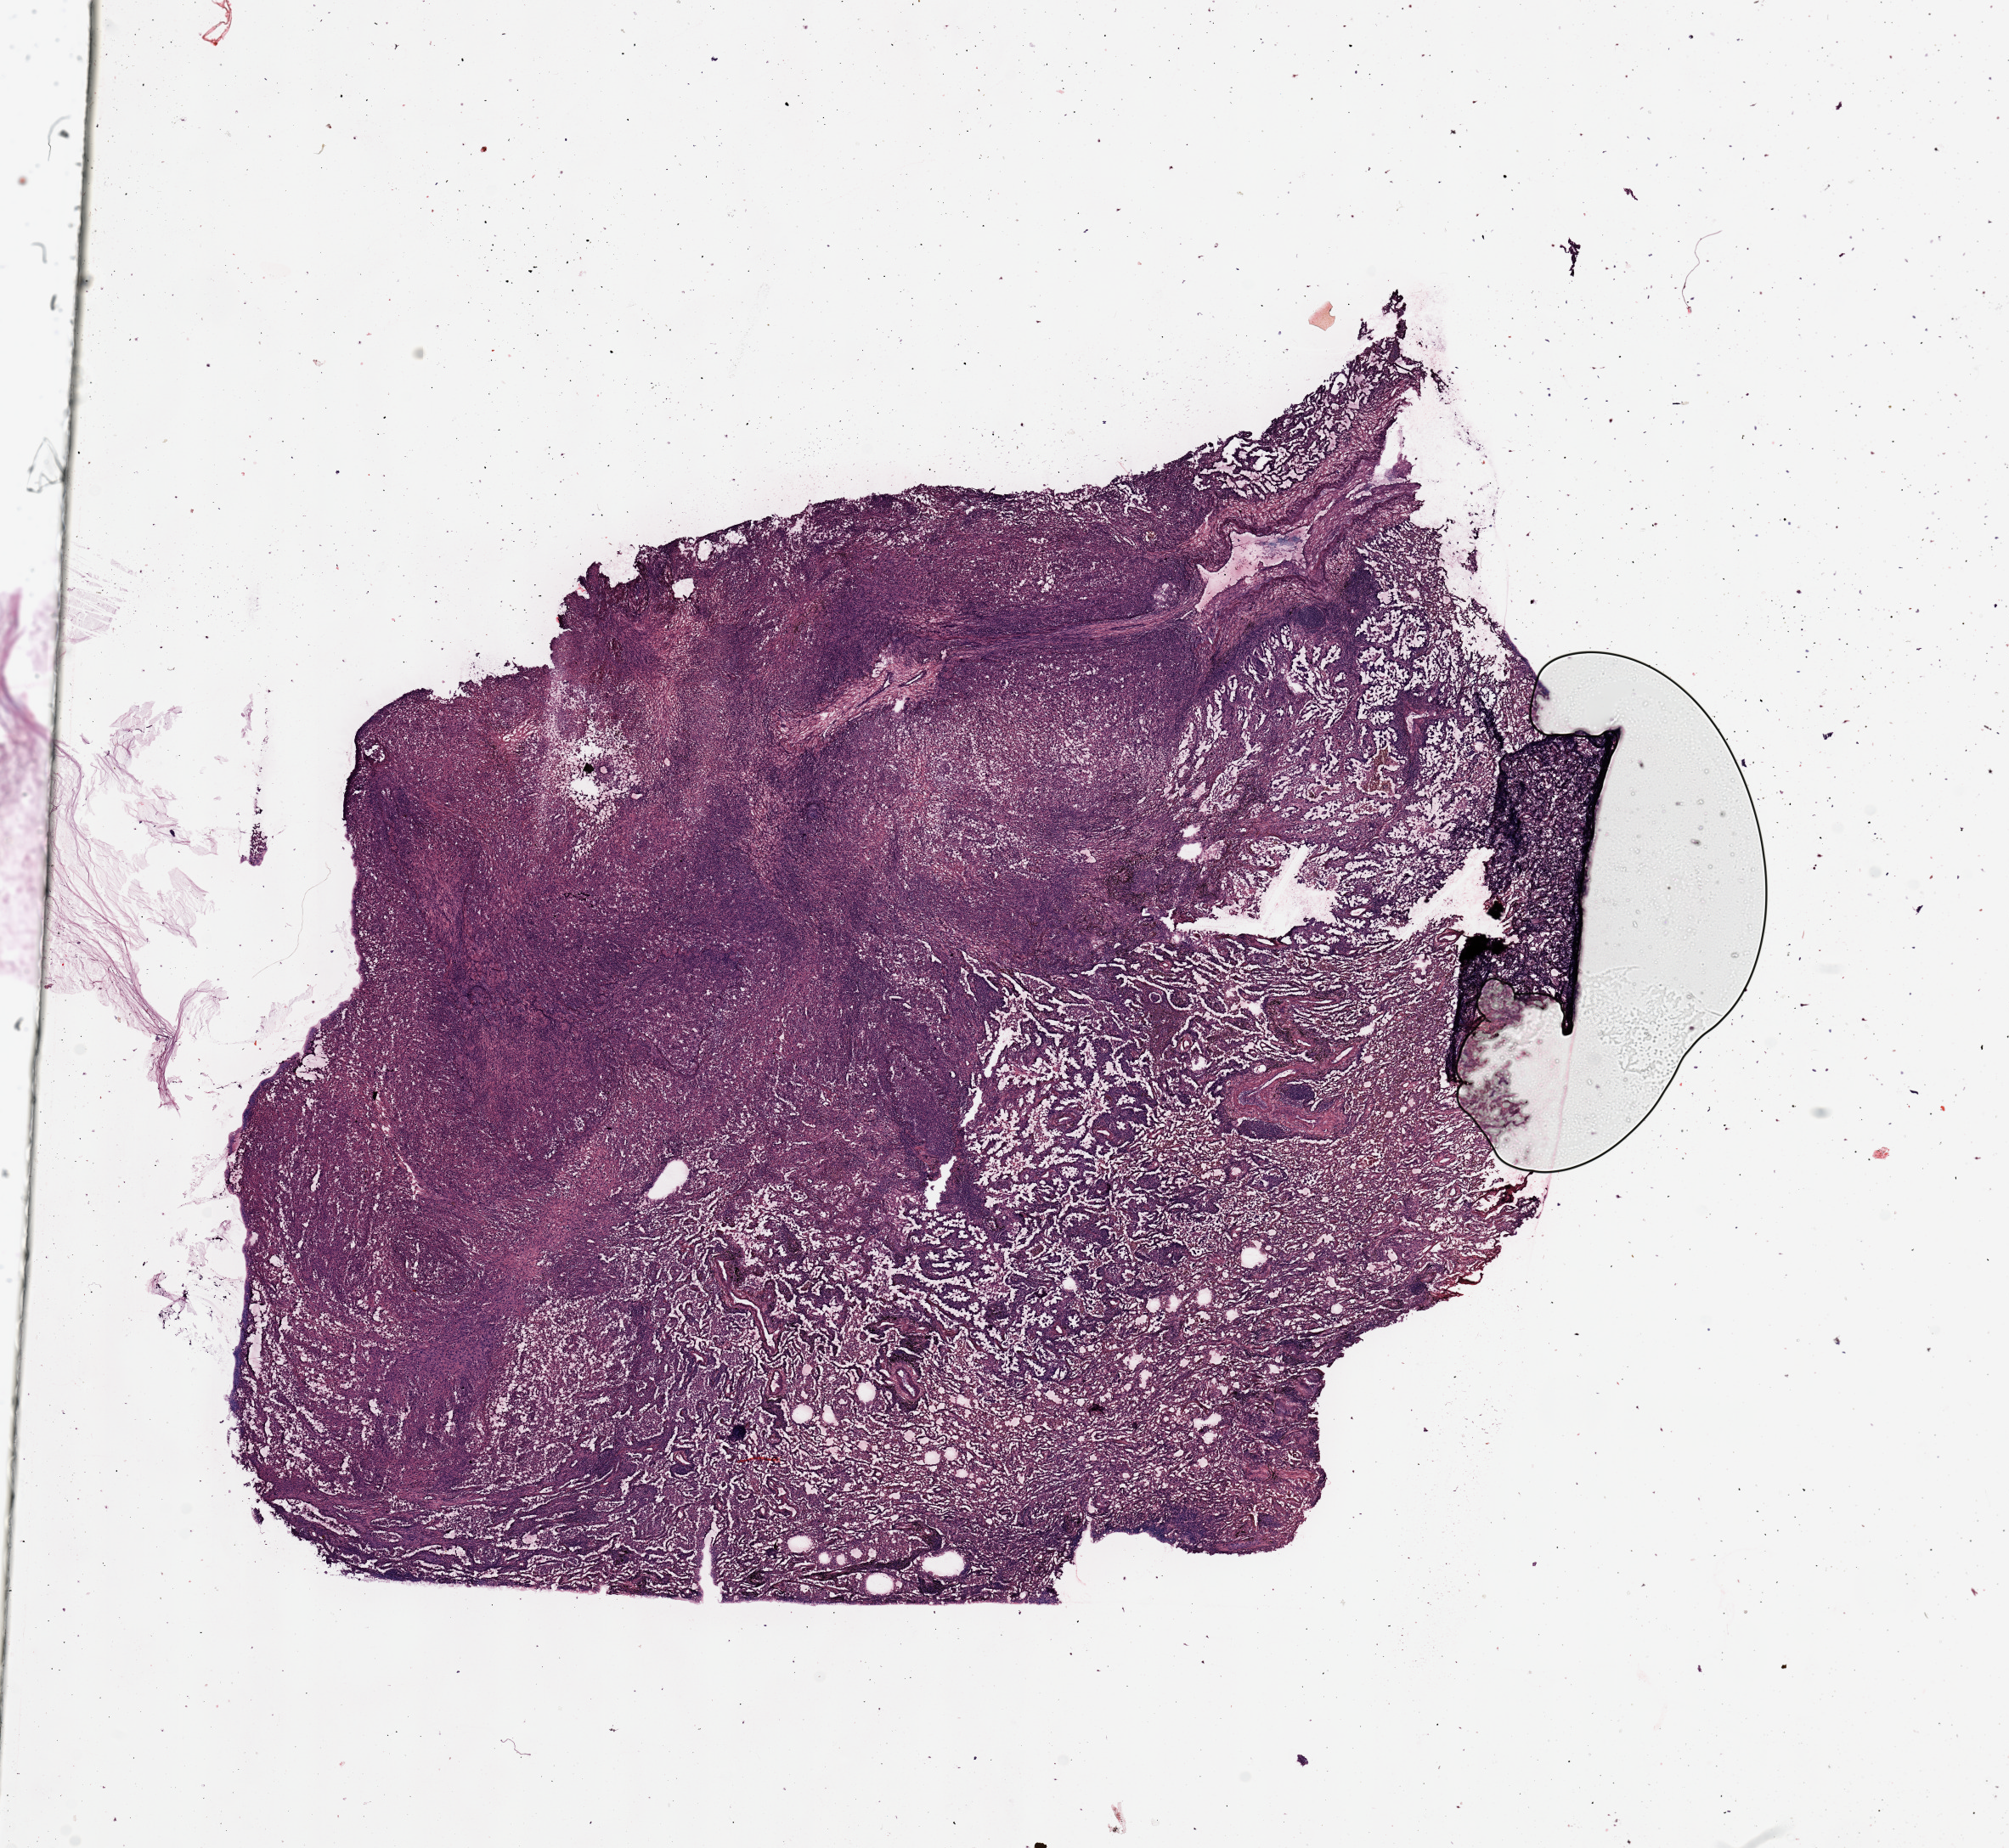
Digitized H&E-stained tissue section (whole slide) — a low-resolution overview of the entire scanned area, about 18.7 x 17.2 mm (slide scanned at 20x); tumour tissue sample, lung. Male, 57 y/o. Histologic grade: G3 (poorly differentiated).
- primary tumour site (as recorded): right upper lobe
- AJCC pathologic stage: IB
- histologic diagnosis: Adenocarcinoma, NOS